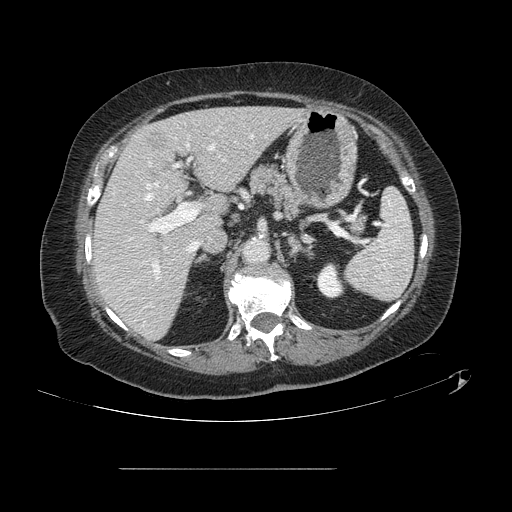
Contrast-enhanced abdominal CT, one axial slice. Position 76 of 148 along the scan axis. 120 kVp. Soft-tissue window (W 400 / L 40 HU). 2.5 mm slice thickness. 512 × 512 image matrix, field of view 439 × 439 mm. Female patient, age 75 years. Case-level facts recorded for this patient, not image findings: diagnosis: colorectal cancer liver metastases, imaged before liver resection; multiple liver metastases: no; largest metastasis: 2.4 cm; chemotherapy before resection: no.
Outlined on this slice (outlined manually by an expert reader):
- hepatic veins: bounding box [x1, y1, x2, y2] px = [146, 145, 214, 251]
- liver: [93, 107, 299, 339]
- planned liver remnant (the part of the liver to remain after resection): [93, 107, 299, 339]
- portal vein (with intrahepatic branches): [131, 133, 254, 275]
- liver metastasis: [148, 136, 163, 154]